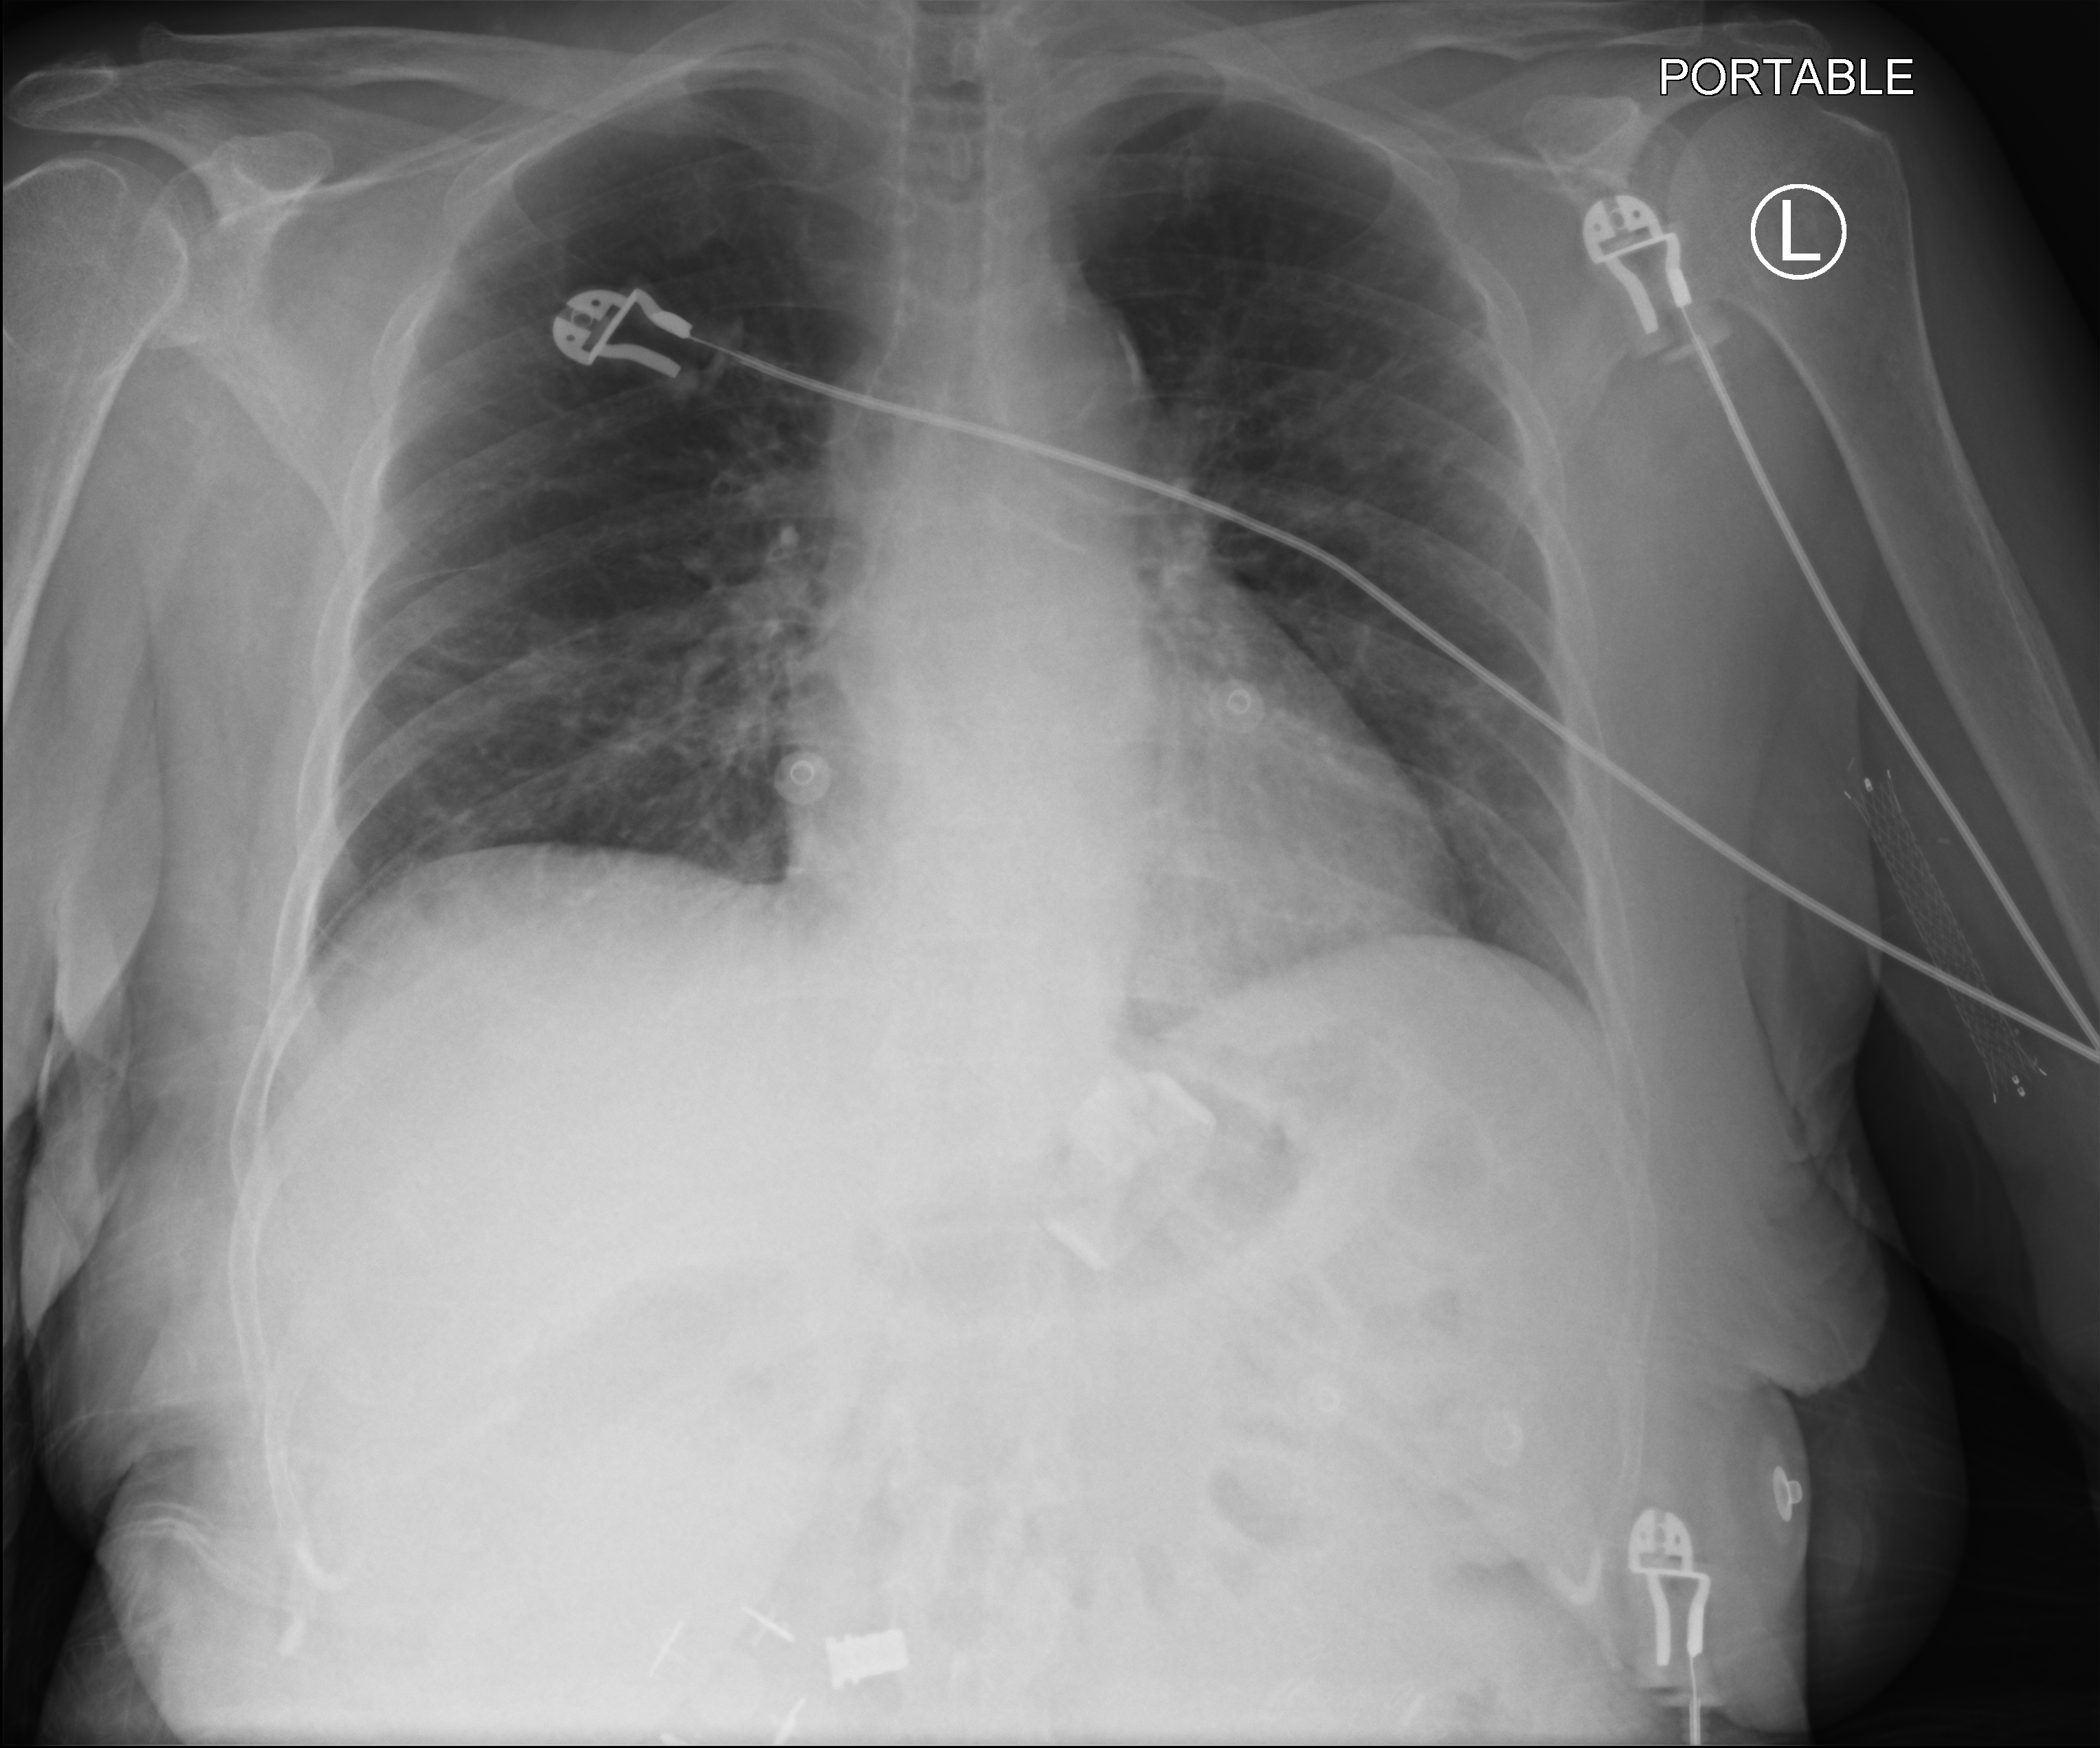
Chest X-ray (portable), anteroposterior (AP) projection. Patient hospitalised with COVID-19; female, aged 60–74 years.
Admission-level facts for this patient (not findings on this image; timing relative to this image not recorded):
- admitted to intensive care during this hospital stay: no
- mechanically ventilated during this hospital stay: no